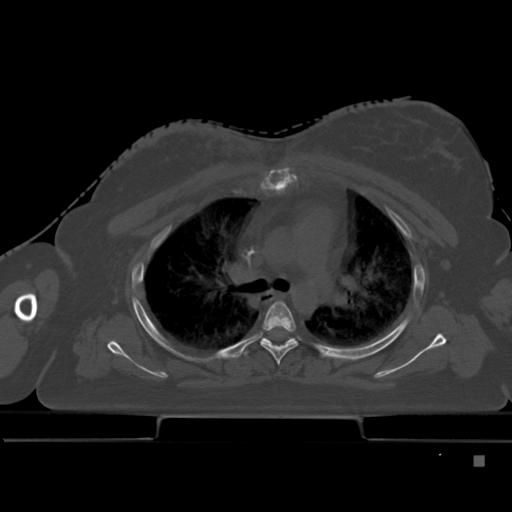
CT including the spine, one axial slice; position 329 of 495 along the scan axis; bone window (W 1800 / L 400 HU); 512 × 512 image matrix, field of view 404 × 404 mm. Female patient, age 33 years. Case-level facts recorded for this patient, not image findings: primary cancer: breast; vertebrae with lytic lesions (as recorded): T1.
Structures marked on this image (semi-automatically segmented with operator editing):
- T4 vertebra: bounding box [x1, y1, x2, y2] px = [261, 301, 298, 366]
- T5 vertebra: [245, 337, 296, 356]